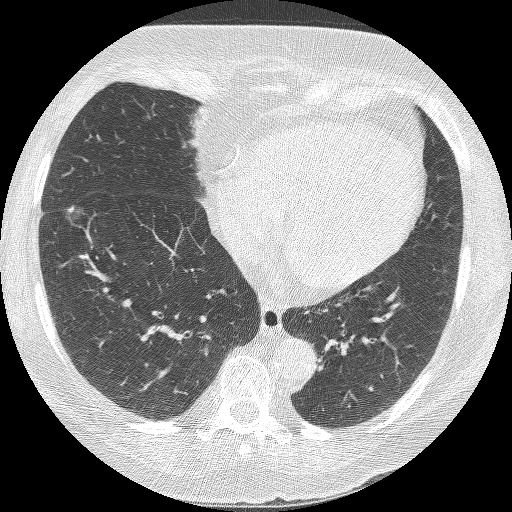
Chest CT (low-dose screening protocol), one axial image. Second annual screen. Lung window (W 1500 / L -600 HU). 512 × 512 image matrix, field of view 310 × 310 mm. Female, age 68 years at enrolment. Current smoker at enrolment.
- Expert-annotated lung lesion, bounding box [x1, y1, x2, y2] px = [34, 194, 93, 251].
- The exam's reader record, not a measurement of the box and not confirmed to be the same lesion: non-calcified nodule or mass ≥4 mm, right lower lobe, 18 × 15 mm, poorly defined margins, ground glass attenuation, pre-existing on the prior screen: yes; interval growth: yes.
- Lung cancer was diagnosed 42 days after this screen: bronchiolo-alveolar adenocarcinoma, NOS, right lower lobe, well differentiated (G1), stage IA (AJCC 6th edition), 13 mm at pathology.